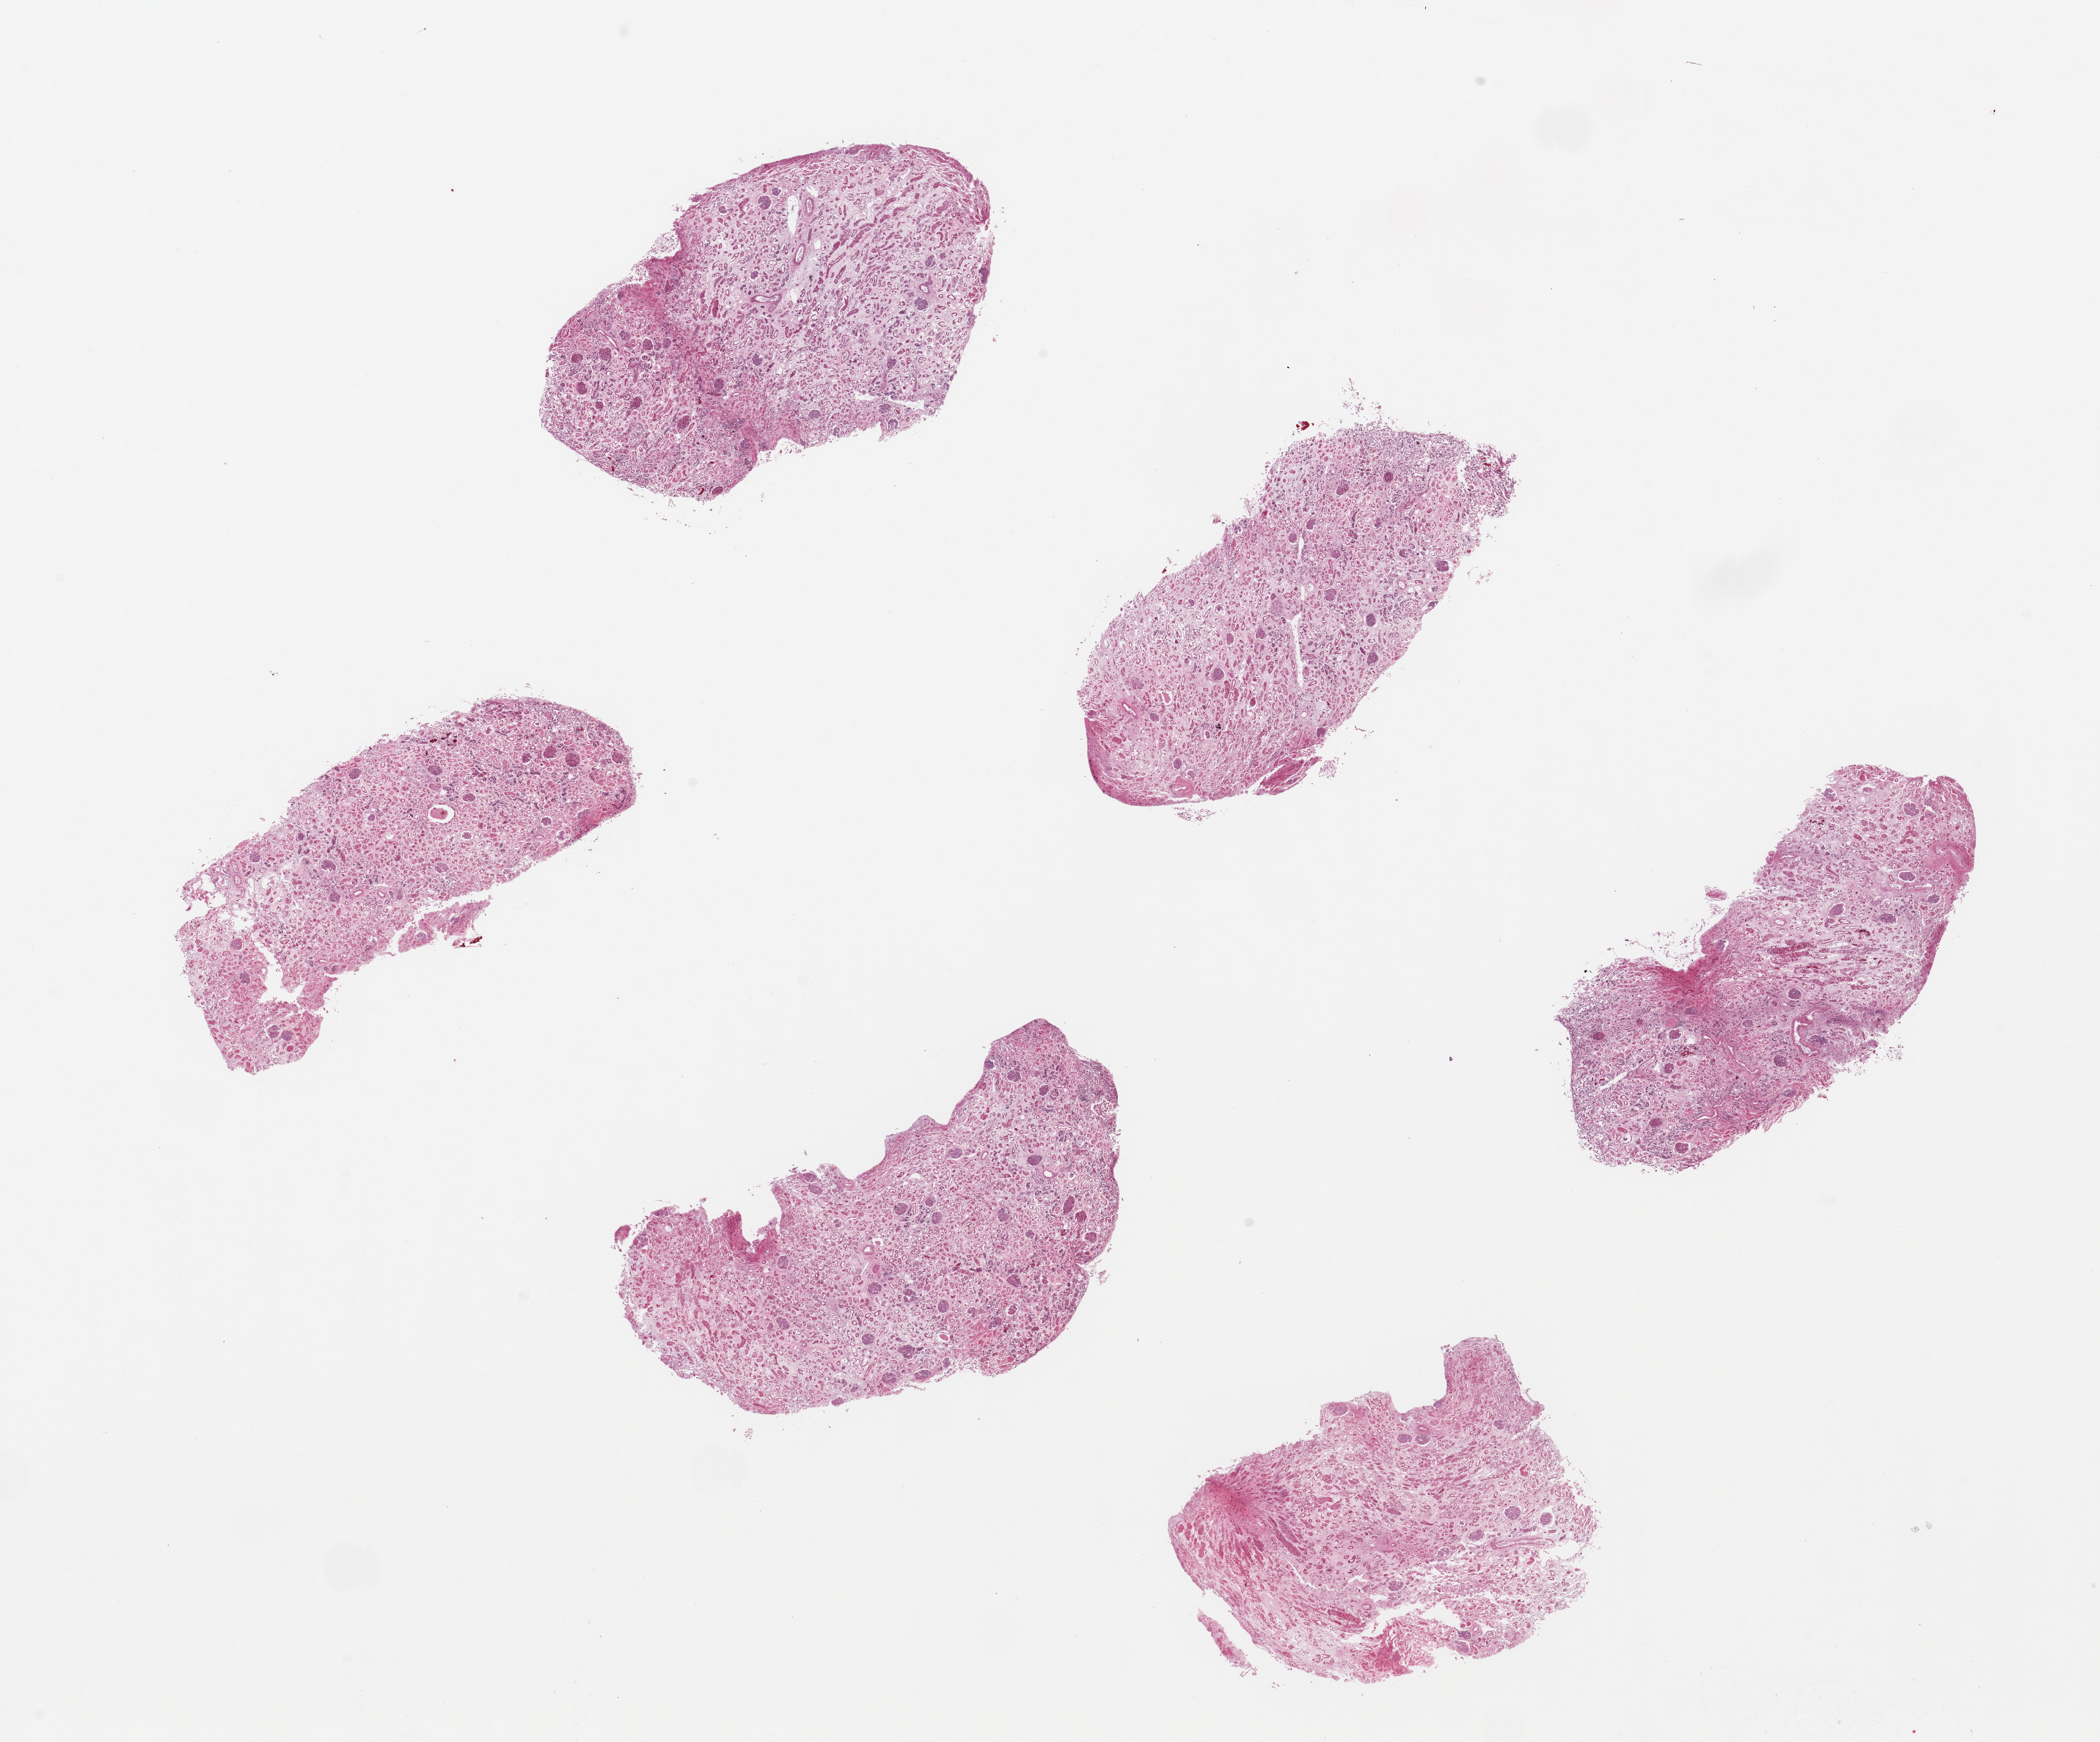
H&E whole-slide image, brightfield, whole scanned area (about 22.6 x 18.8 mm, acquisition: 20x scan) shown as a low-resolution overview; PAXgene-fixed paraffin-embedded (PFPE) section; section of renal cortex (target tissue); tissue donor sample.
Pathologist's review note for this sample: 6 pieces ~ 5x2mmbadly autolyzed.